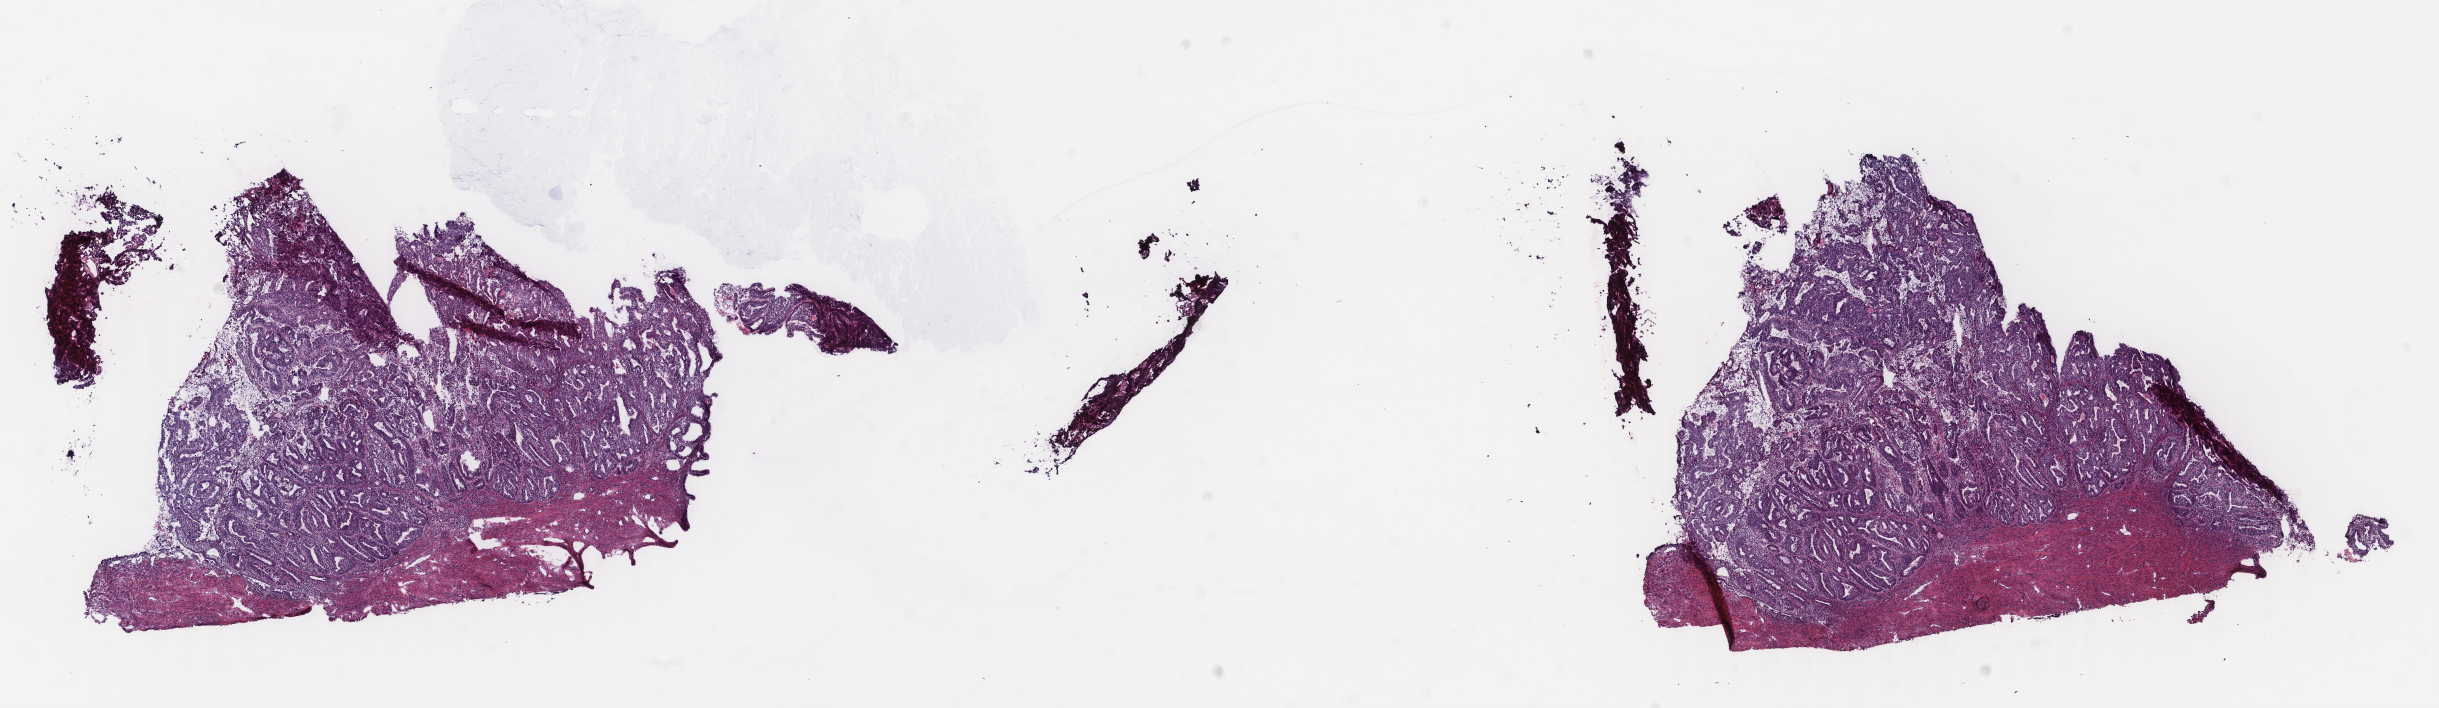
Digitized Hematoxylin and eosin (H&E) stained tissue section (whole slide), shown as a low-resolution overview of the whole scanned area (about 19.4 x 5.6 mm, slide scanned at 40x). Frozen section. Primary tumour sample from the uterus. Female, age 87 years at initial diagnosis. Histologic grade: G1 (well differentiated). Pathologist review of this section (percent, as recorded): tumour cells 80%, tumour nuclei 80%, normal cells 0%, stromal cells 15%, necrosis 5%. Inflammatory infiltration, as recorded: lymphocyte infiltration 40%, monocyte infiltration 30%, neutrophil infiltration 20%.
Histologic diagnosis: Endometrioid adenocarcinoma, NOS (endometrium). FIGO stage: IB.